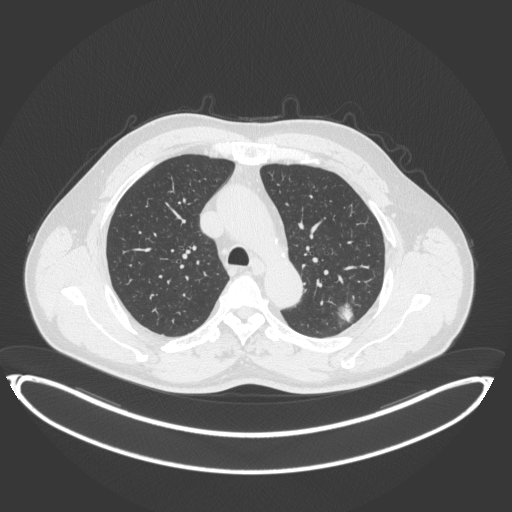
Chest CT, one axial slice; position 259 of 399 along the scan axis; reconstruction kernel B31f; lung window (W 1500 / L -600 HU); 1 mm slice thickness; 512 × 512 image matrix, field of view 469 × 469 mm. Male patient, age 58 years. Case-level facts recorded for this patient, not image findings: clinical TNM (as recorded): T1c N0 M0.
Structures marked on this image (bounding box drawn by a radiologist):
- lung tumour (recorded histology: adenocarcinoma): box from (x=334, y=297) to (x=358, y=325) px